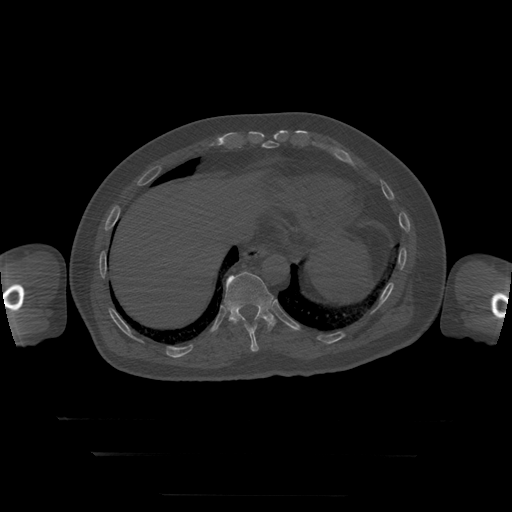
CT including the spine, one axial slice; slice 110 of 397 in the series (ordered by position); bone window (W 1800 / L 400 HU); 1.25 mm slice thickness; 512 × 512 image matrix, field of view 510 × 510 mm. Patient age 73 years. From the clinical record (not read from this slice): primary cancer: prostate.
Annotated regions visible in this slice (semi-automatically segmented with operator editing):
- T10 vertebra: bounding box [x1, y1, x2, y2] px = [230, 320, 268, 352]
- T11 vertebra: [224, 272, 276, 330]